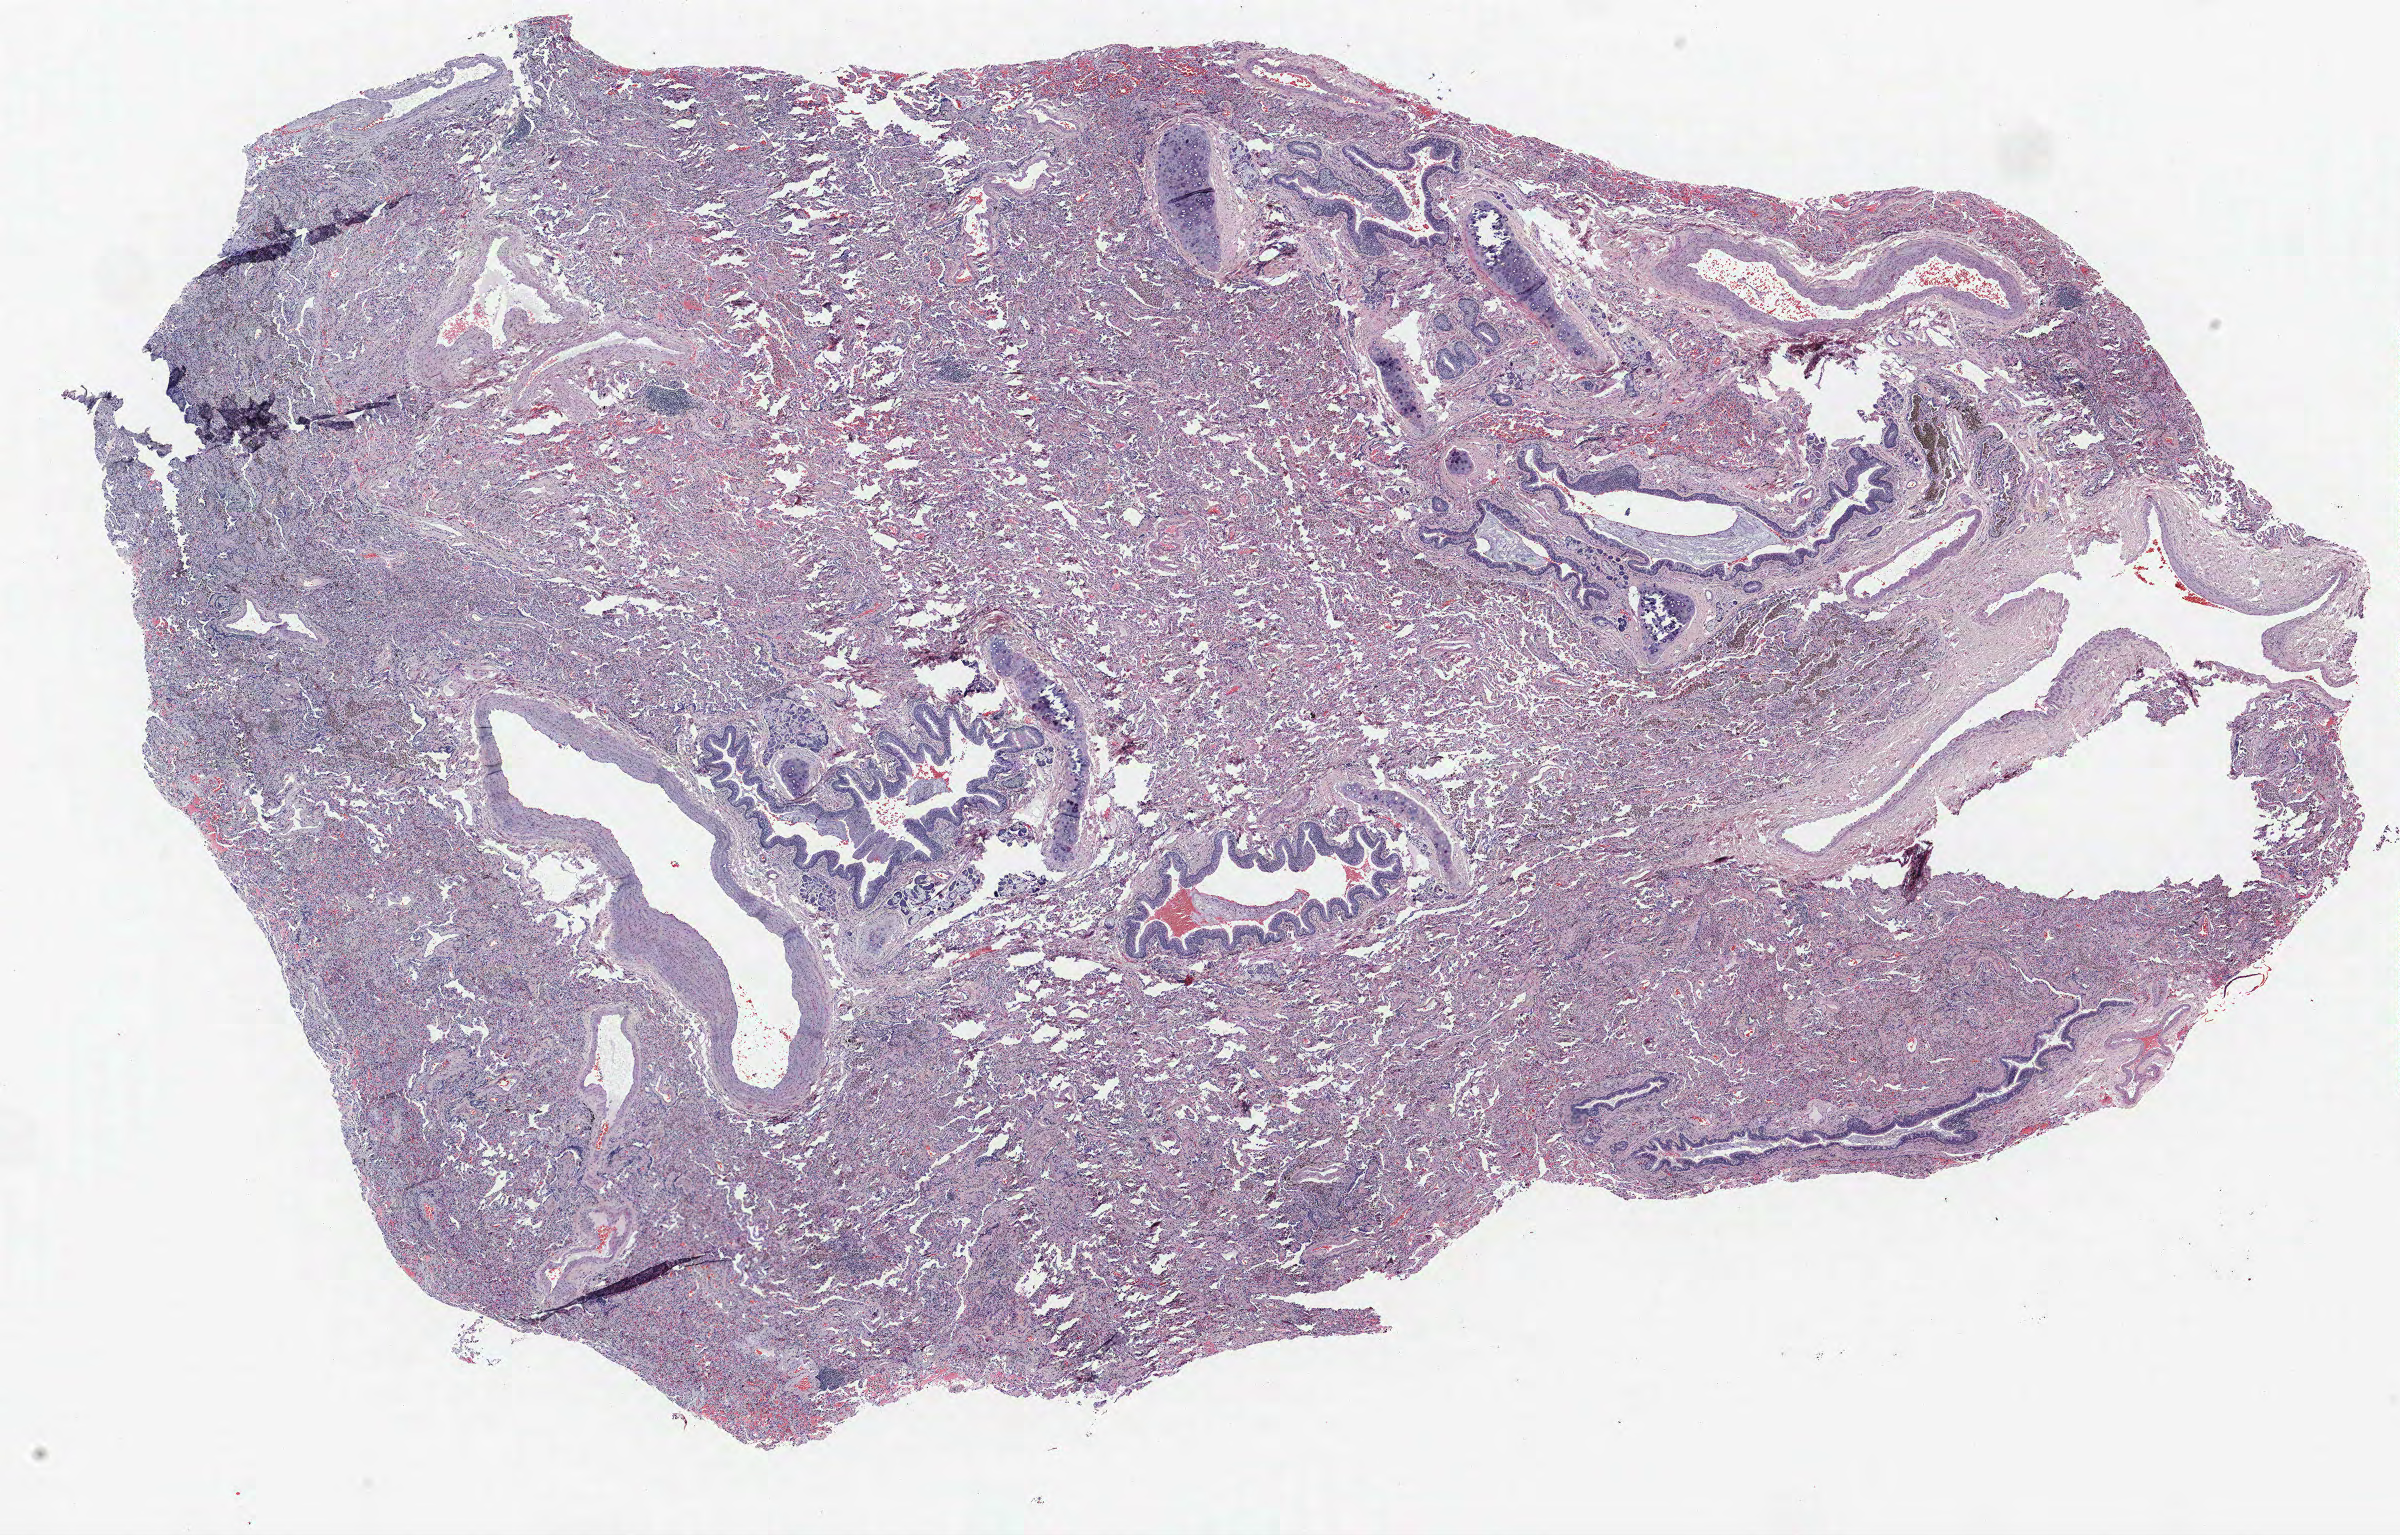
Hematoxylin and eosin (H&E) stained whole-slide image, whole scanned area (about 19.2 x 12.3 mm) shown as a low-resolution overview, formalin-fixed paraffin-embedded (FFPE) section, lung. Female patient, aged 61 at enrolment. Current smoker at enrolment.
Participant's lung-cancer diagnosis: Adenocarcinoma, NOS.